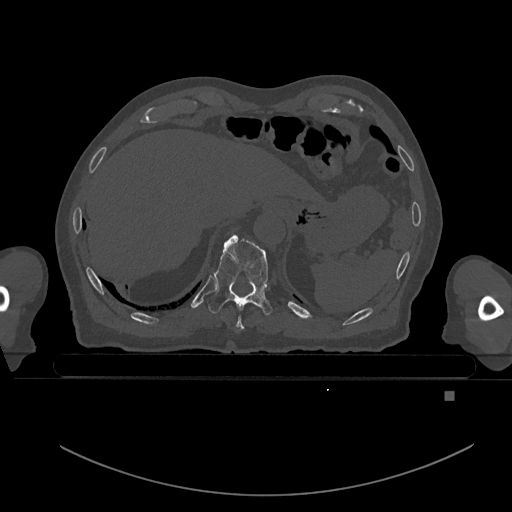
CT including the spine, one axial slice. Slice 94 of 969 in the series (ordered by position). Bone window (W 1800 / L 400 HU). 0.5 mm slice thickness. 512 × 512 image matrix. Male patient, age 82 years. Case-level facts recorded for this patient, not image findings: primary cancer: prostate.
Structures marked on this image (semi-automatically segmented with operator editing):
- T10 vertebra: bounding box (x1, y1, x2, y2) in pixels: (208, 234, 273, 316)
- T9 vertebra: (235, 316, 244, 330)